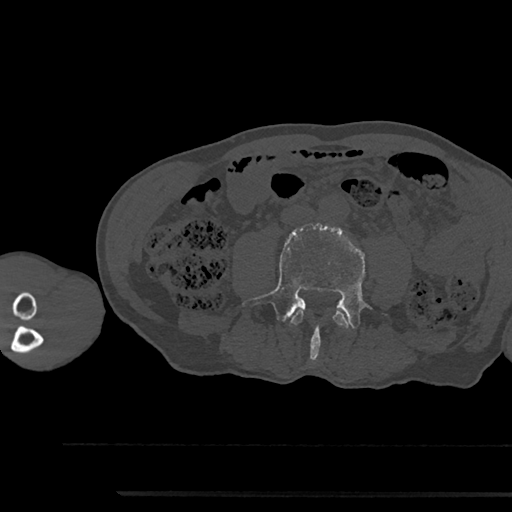
CT including the spine, one axial slice. Slice 431 of 797 in the series (ordered by position). Reconstruction kernel Br40s/3. Bone window (W 1800 / L 400 HU). 0.5 mm slice thickness. 512 × 512 image matrix, field of view 367 × 367 mm. Male patient, age 79 years. Case-level facts recorded for this patient, not image findings: primary cancer: prostate.
Structures marked on this image (semi-automatic segmentation, software-assisted and operator-edited):
- L3 vertebra: bounding box <291,311,349,328> (left, top, right, bottom; pixels)
- L4 vertebra: <243,224,370,360>